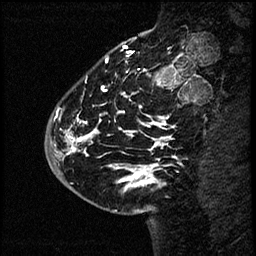
Breast MRI (dynamic contrast-enhanced), one sagittal slice; position 18 of 60 along the scan axis; dynamic contrast-enhanced study with each time point stored as its own series, time point 2 of 4 at this slice position (early post-contrast, ordered by acquisition time); 1.5 T; TE 4.2 ms, TR 17.6 ms; 256 × 256 image matrix, field of view 200 × 200 mm. Female patient, age 43 years. Case-level facts recorded for this patient, not image findings: setting: breast cancer imaged before/during neoadjuvant chemotherapy.
Outlined on this slice (semi-automatically segmented with operator editing):
- analysis volume of interest (the breast-tissue region the enhancement analysis was run in; not a lesion): box from (x=50, y=58) to (x=169, y=191) px
- tumour enhancement mask (voxels above the 100 % enhancement threshold inside the analysis volume of interest): (x=54, y=81)–(x=169, y=185)